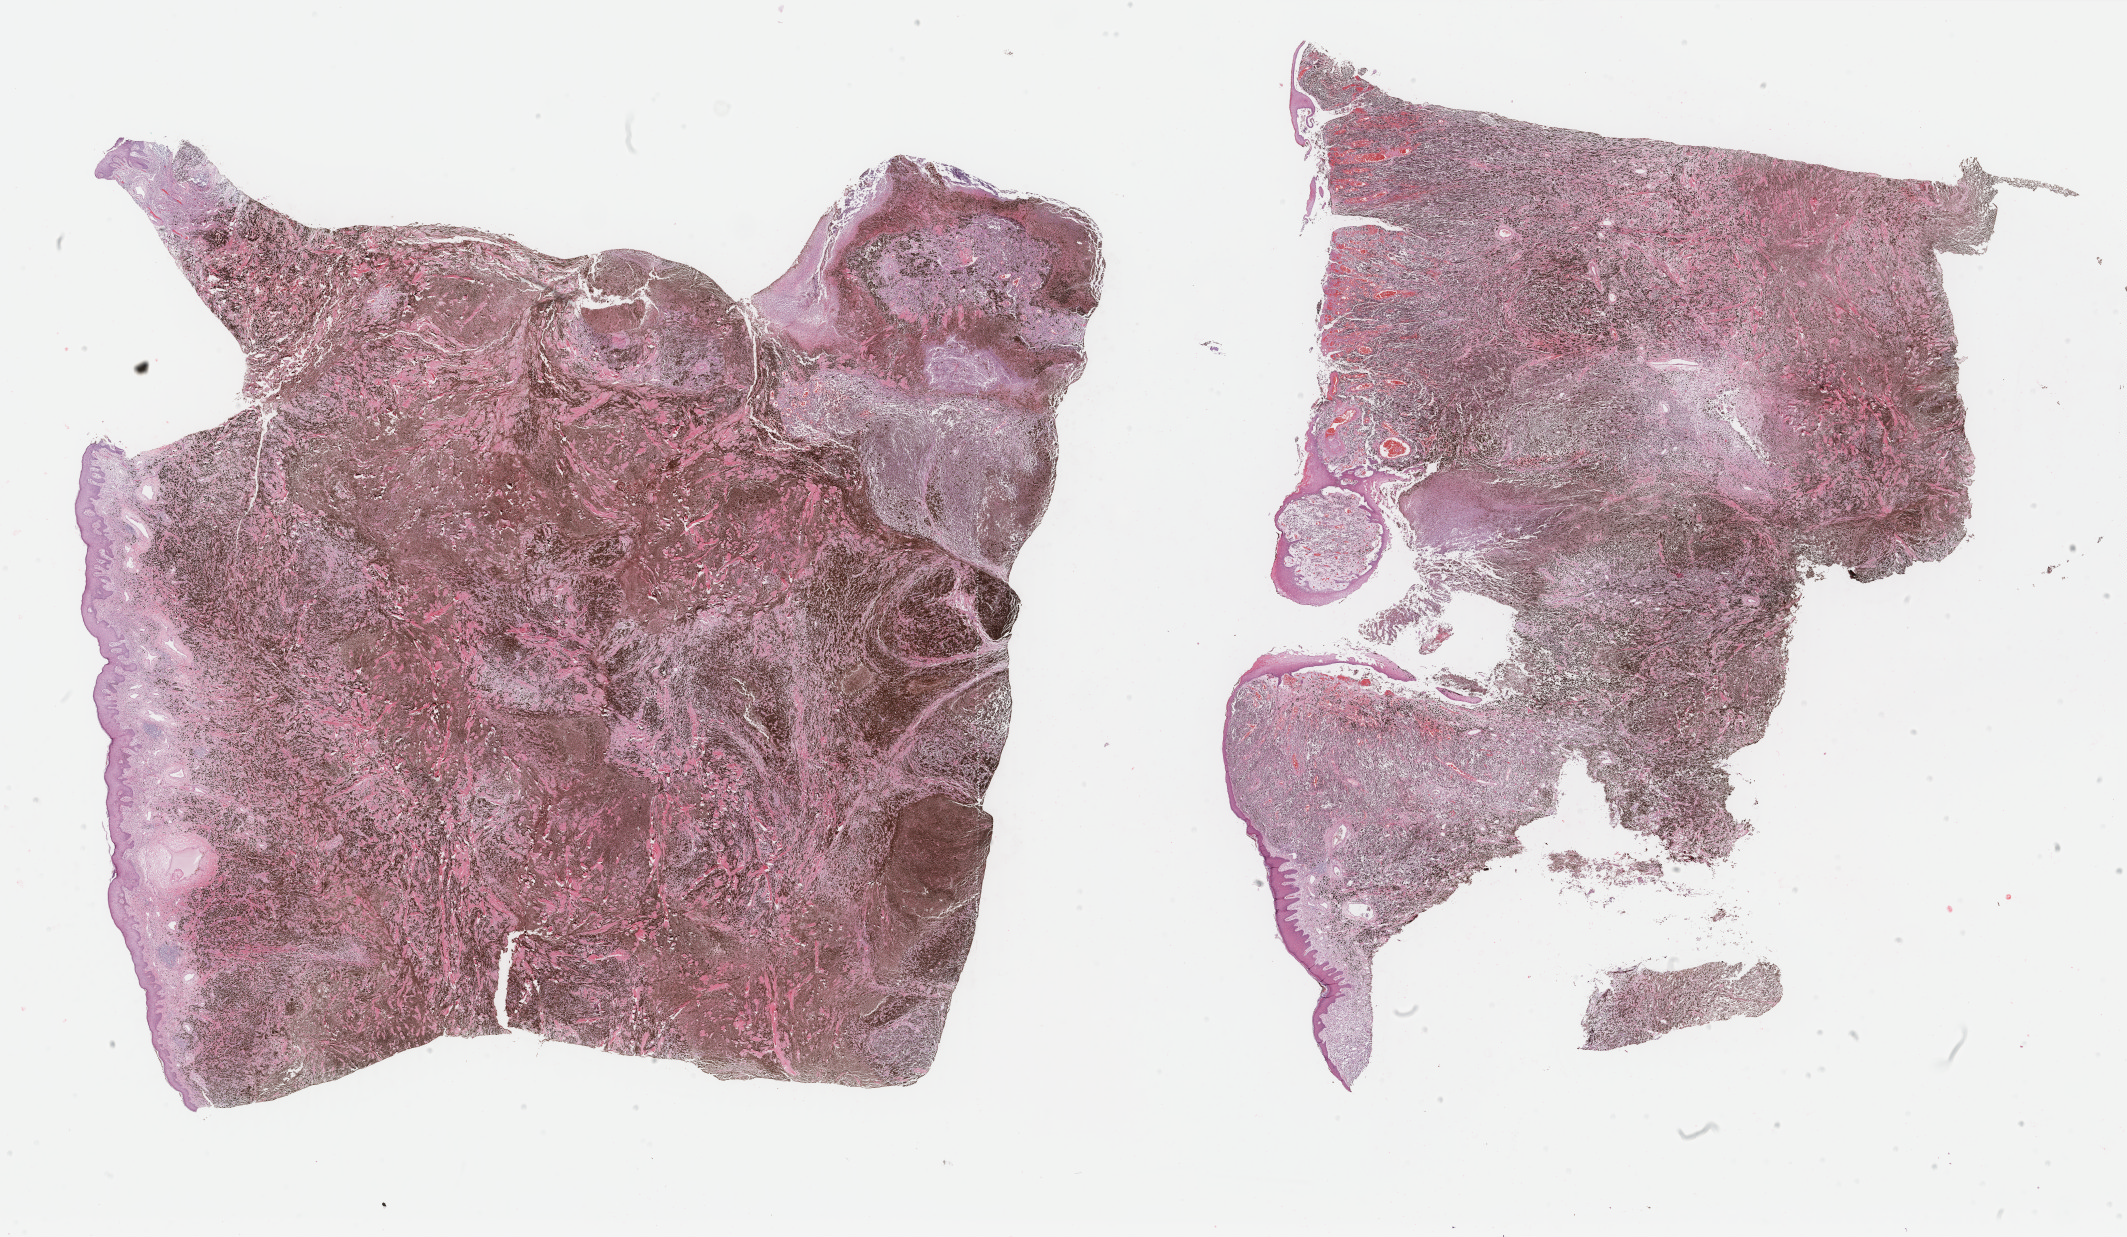
Digitized H&E-stained tissue section (whole slide) — low-resolution overview of the scanned area, about 33.8 x 19.6 mm, formalin-fixed paraffin-embedded (FFPE) diagnostic section, primary tumour sample from the skin. Patient: male, age at initial diagnosis 70 years.
Diagnosis: Superficial spreading melanoma. AJCC pathologic stage: IIIC (6th edition). TNM: T4b N3 M0.